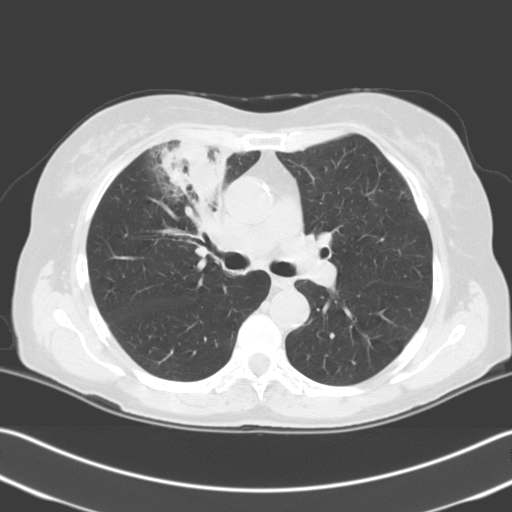
Low-dose screening chest CT, one axial slice; position 134 of 204 along the scan axis; 140 kVp; lung window (W 1500 / L -600 HU); 512 × 512 image matrix, field of view 348 × 348 mm.
Annotated regions visible in this slice (expert manual segmentation):
- lesion 1 (tumor, upper lobe of right lung): bounding box [x1, y1, x2, y2] px = [160, 137, 231, 211]